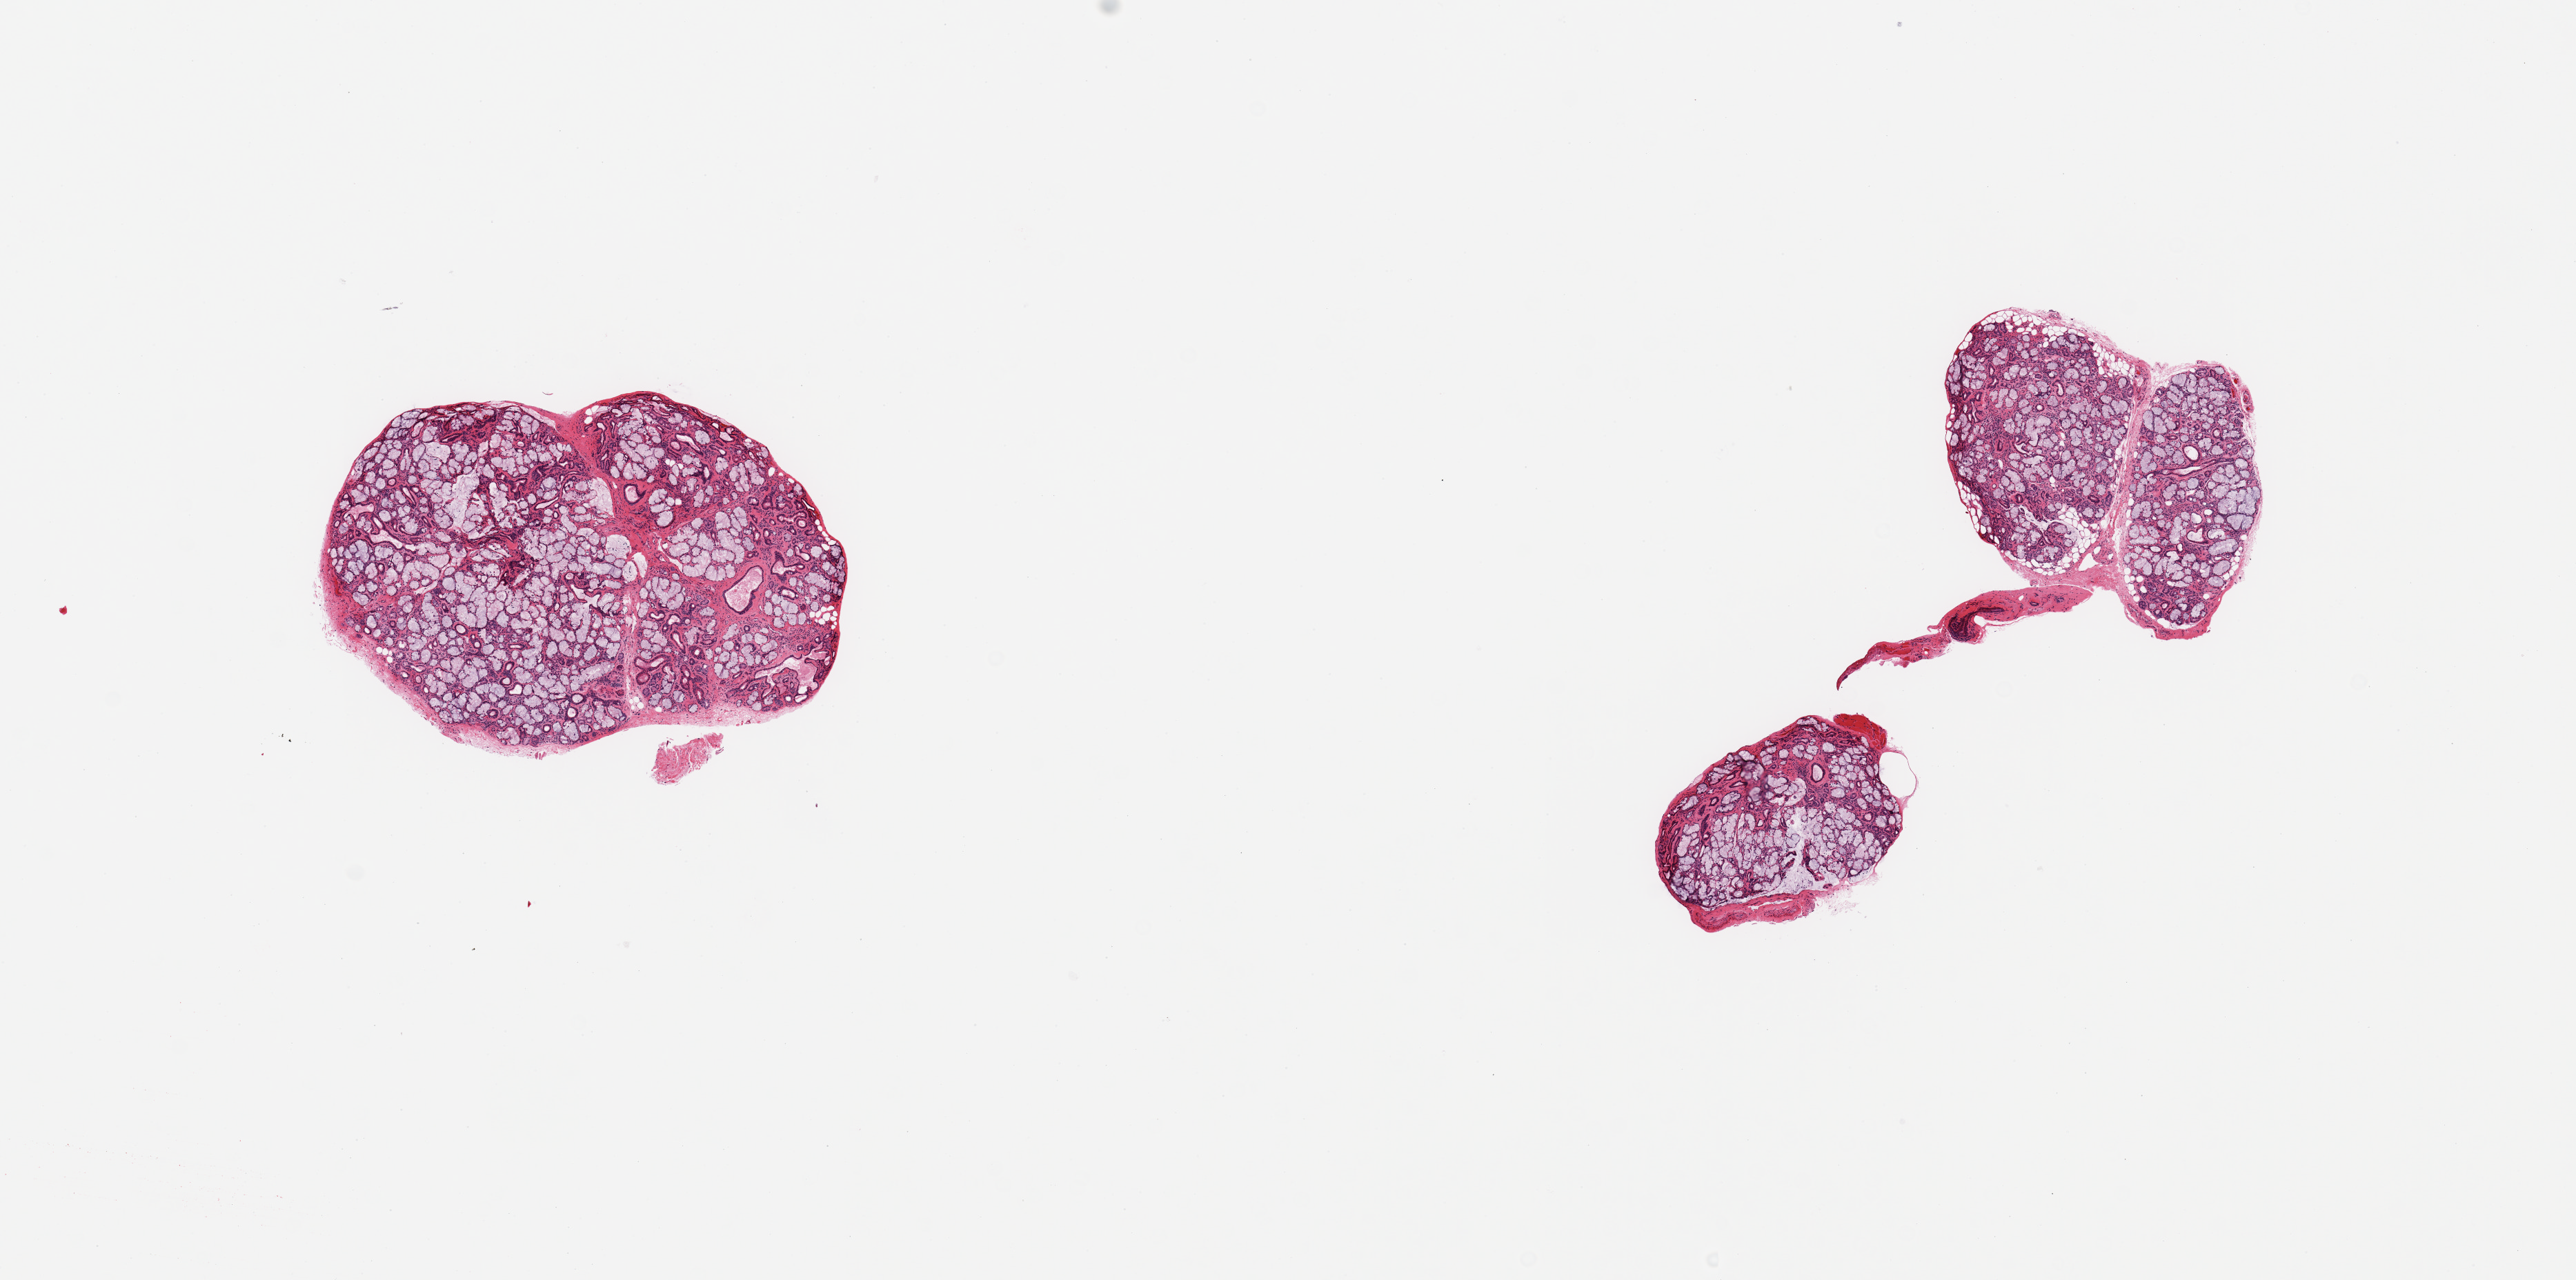
Hematoxylin and eosin (H&E) whole-slide image, brightfield — shown as a low-resolution overview of the whole scanned area (about 14.8 x 7.3 mm, acquisition: 20x scan); PAXgene-fixed paraffin-embedded (PFPE) section; sampled site (target tissue): minor salivary gland; donor tissue sample. Male donor.
Review note (as recorded): 3 pieces, >95% glandular elements; excellent specimen.